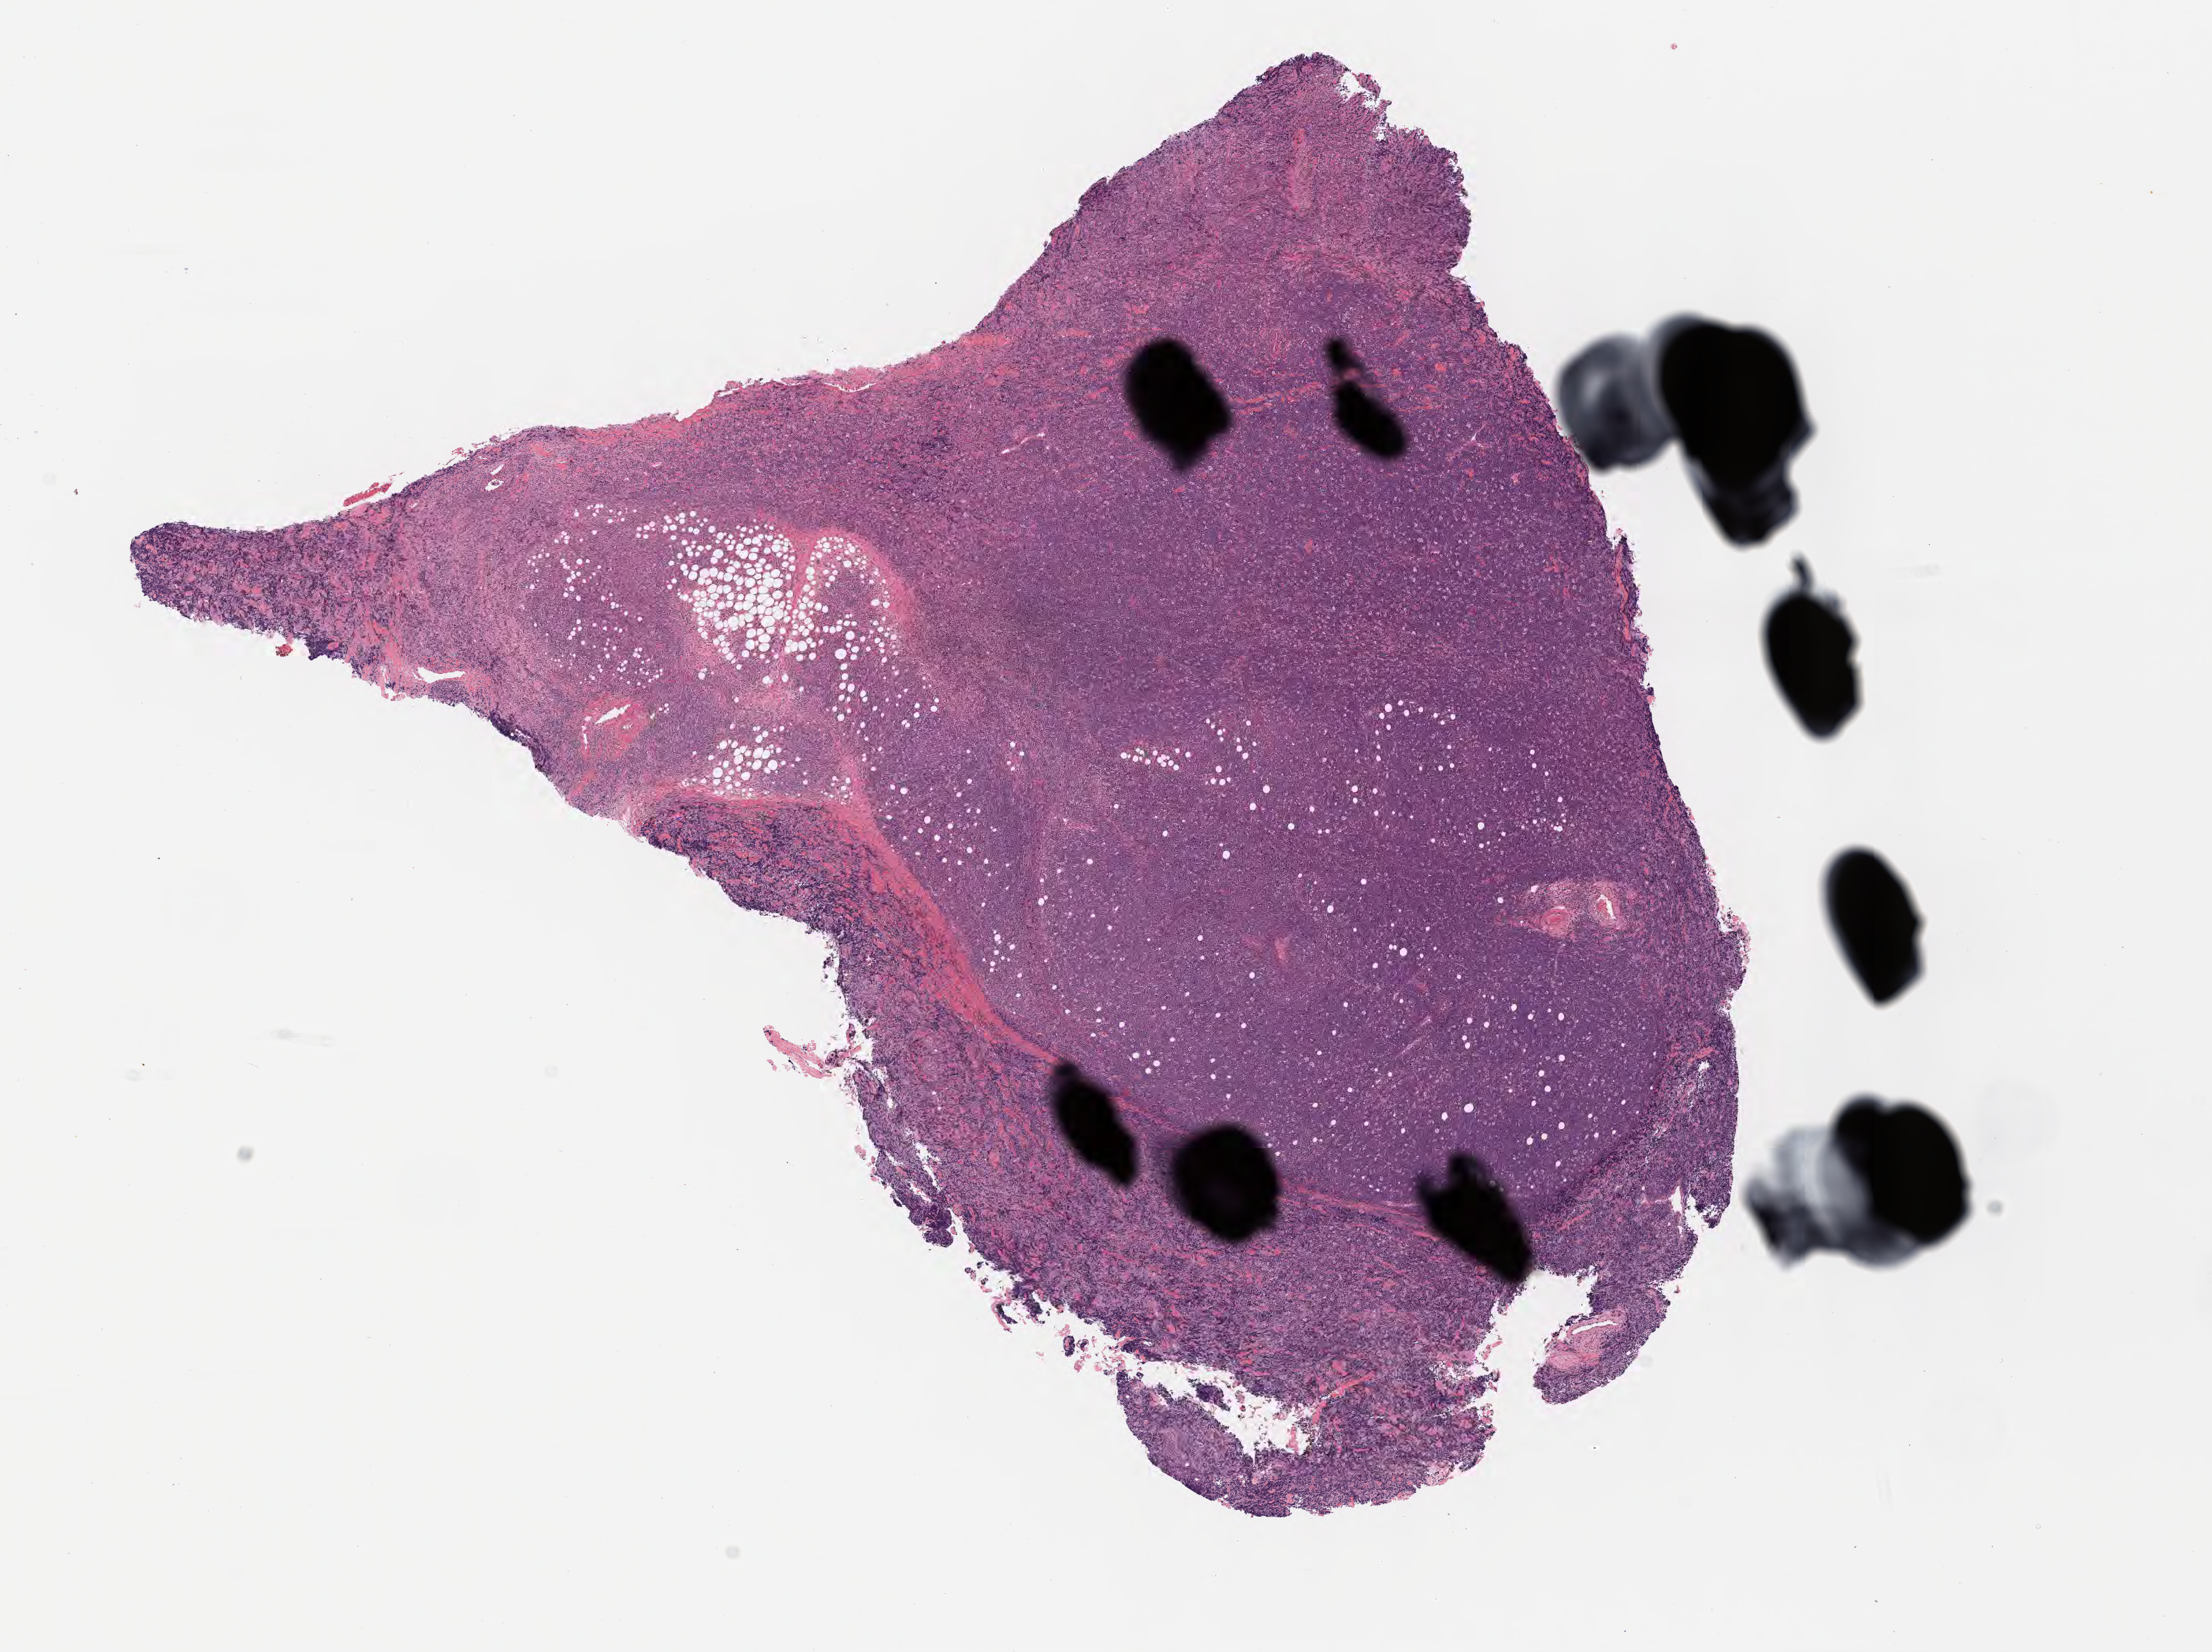
Whole-slide image, haematoxylin and eosin stain — low-resolution overview of the scanned area, about 13.1 x 9.8 mm; tumor tissue; site: lymph node of head and neck. Patient male; age 25 years.
Diagnosis: Malignant lymphoma, non-Hodgkin, NOS.